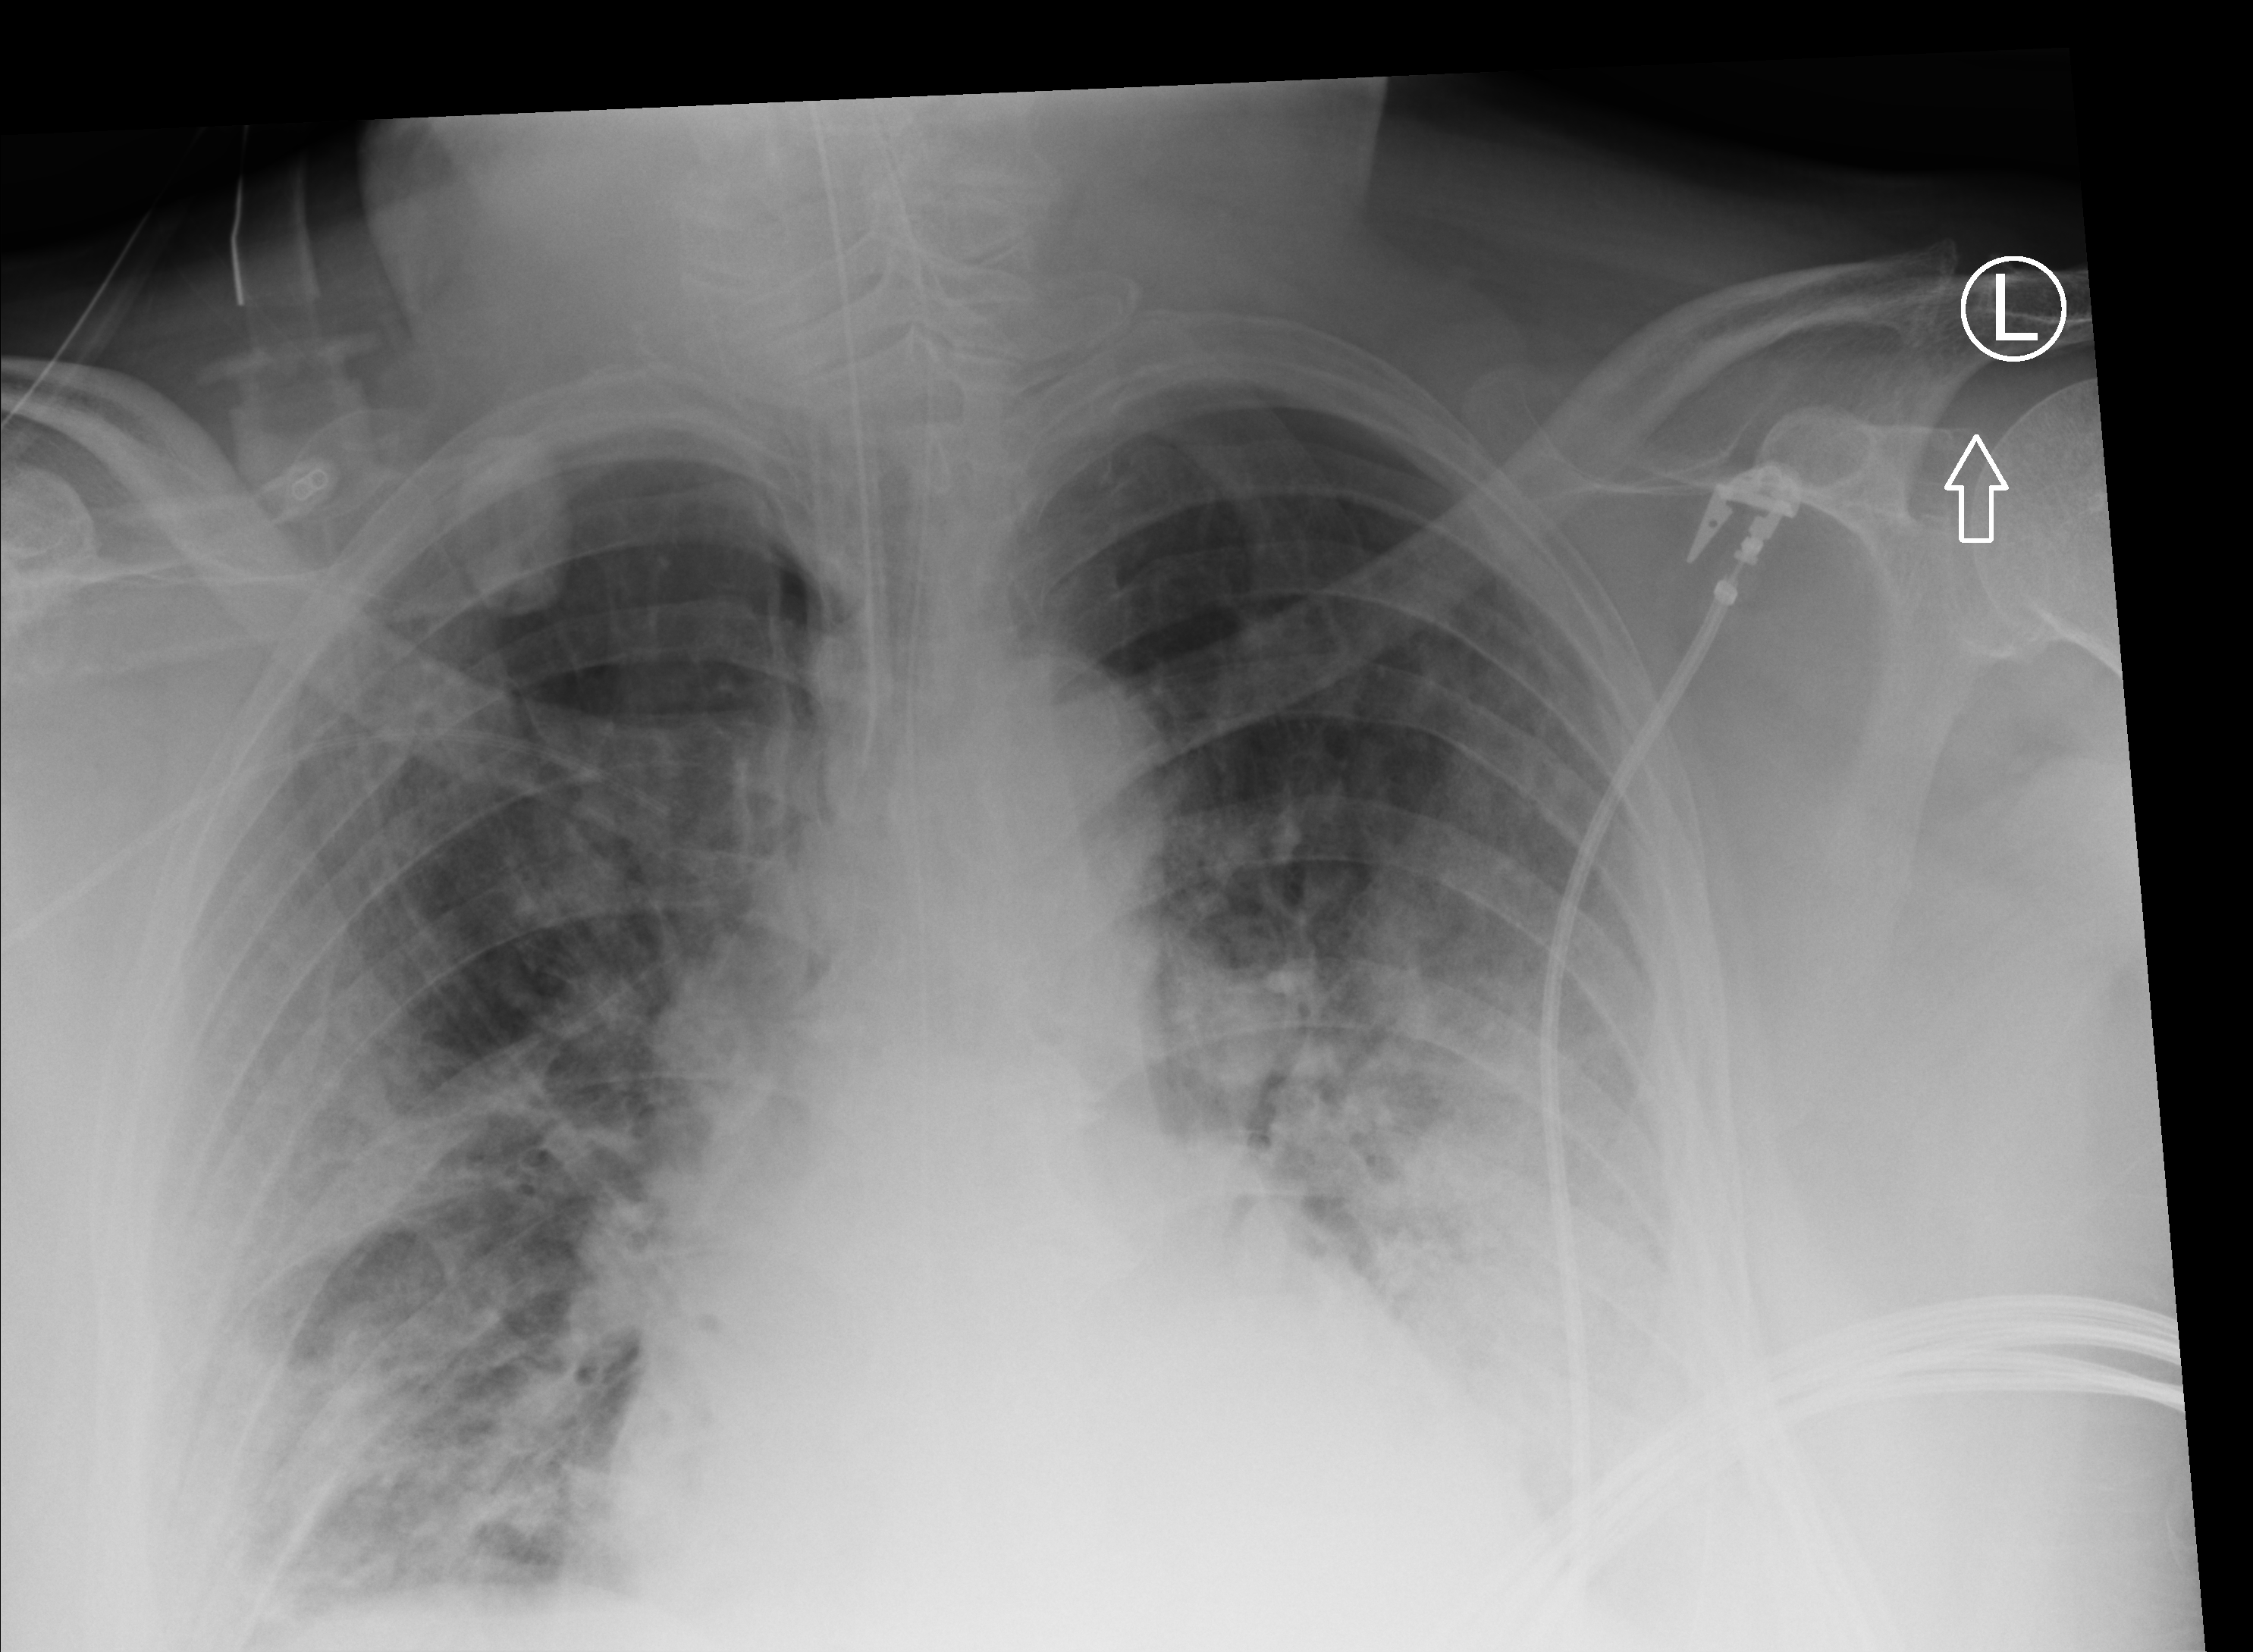
Chest X-ray (portable). Male patient hospitalised with COVID-19, age 60–74 years.
Hospital-stay facts (about this admission, not read from this image; timing relative to this image not recorded): length of hospital stay: 20 days; smoking status (admission record): former; admitted to intensive care during this hospital stay: yes.